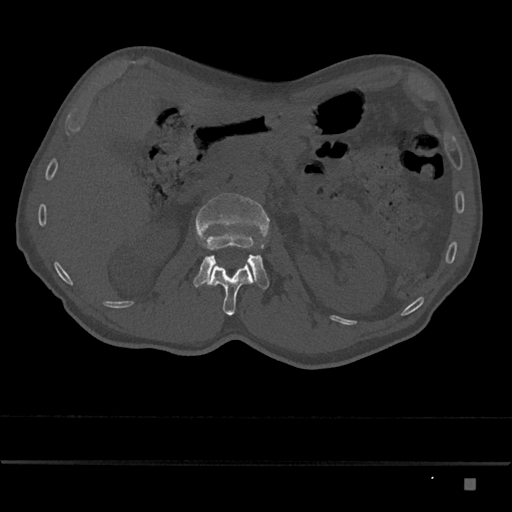
CT including the spine, one axial slice. Position 513 of 797 along the scan axis. Reconstruction kernel Br40s/3. 120 kVp. Bone window (W 1800 / L 400 HU). 512 × 512 image matrix. Male patient, age 72 years. From the clinical record (not read from this slice): primary cancer: prostate.
Structures marked on this image (semi-automatic segmentation, software-assisted and operator-edited):
- L1 vertebra: bounding box <207,262,255,316> (left, top, right, bottom; pixels)
- L2 vertebra: <193,193,270,289>